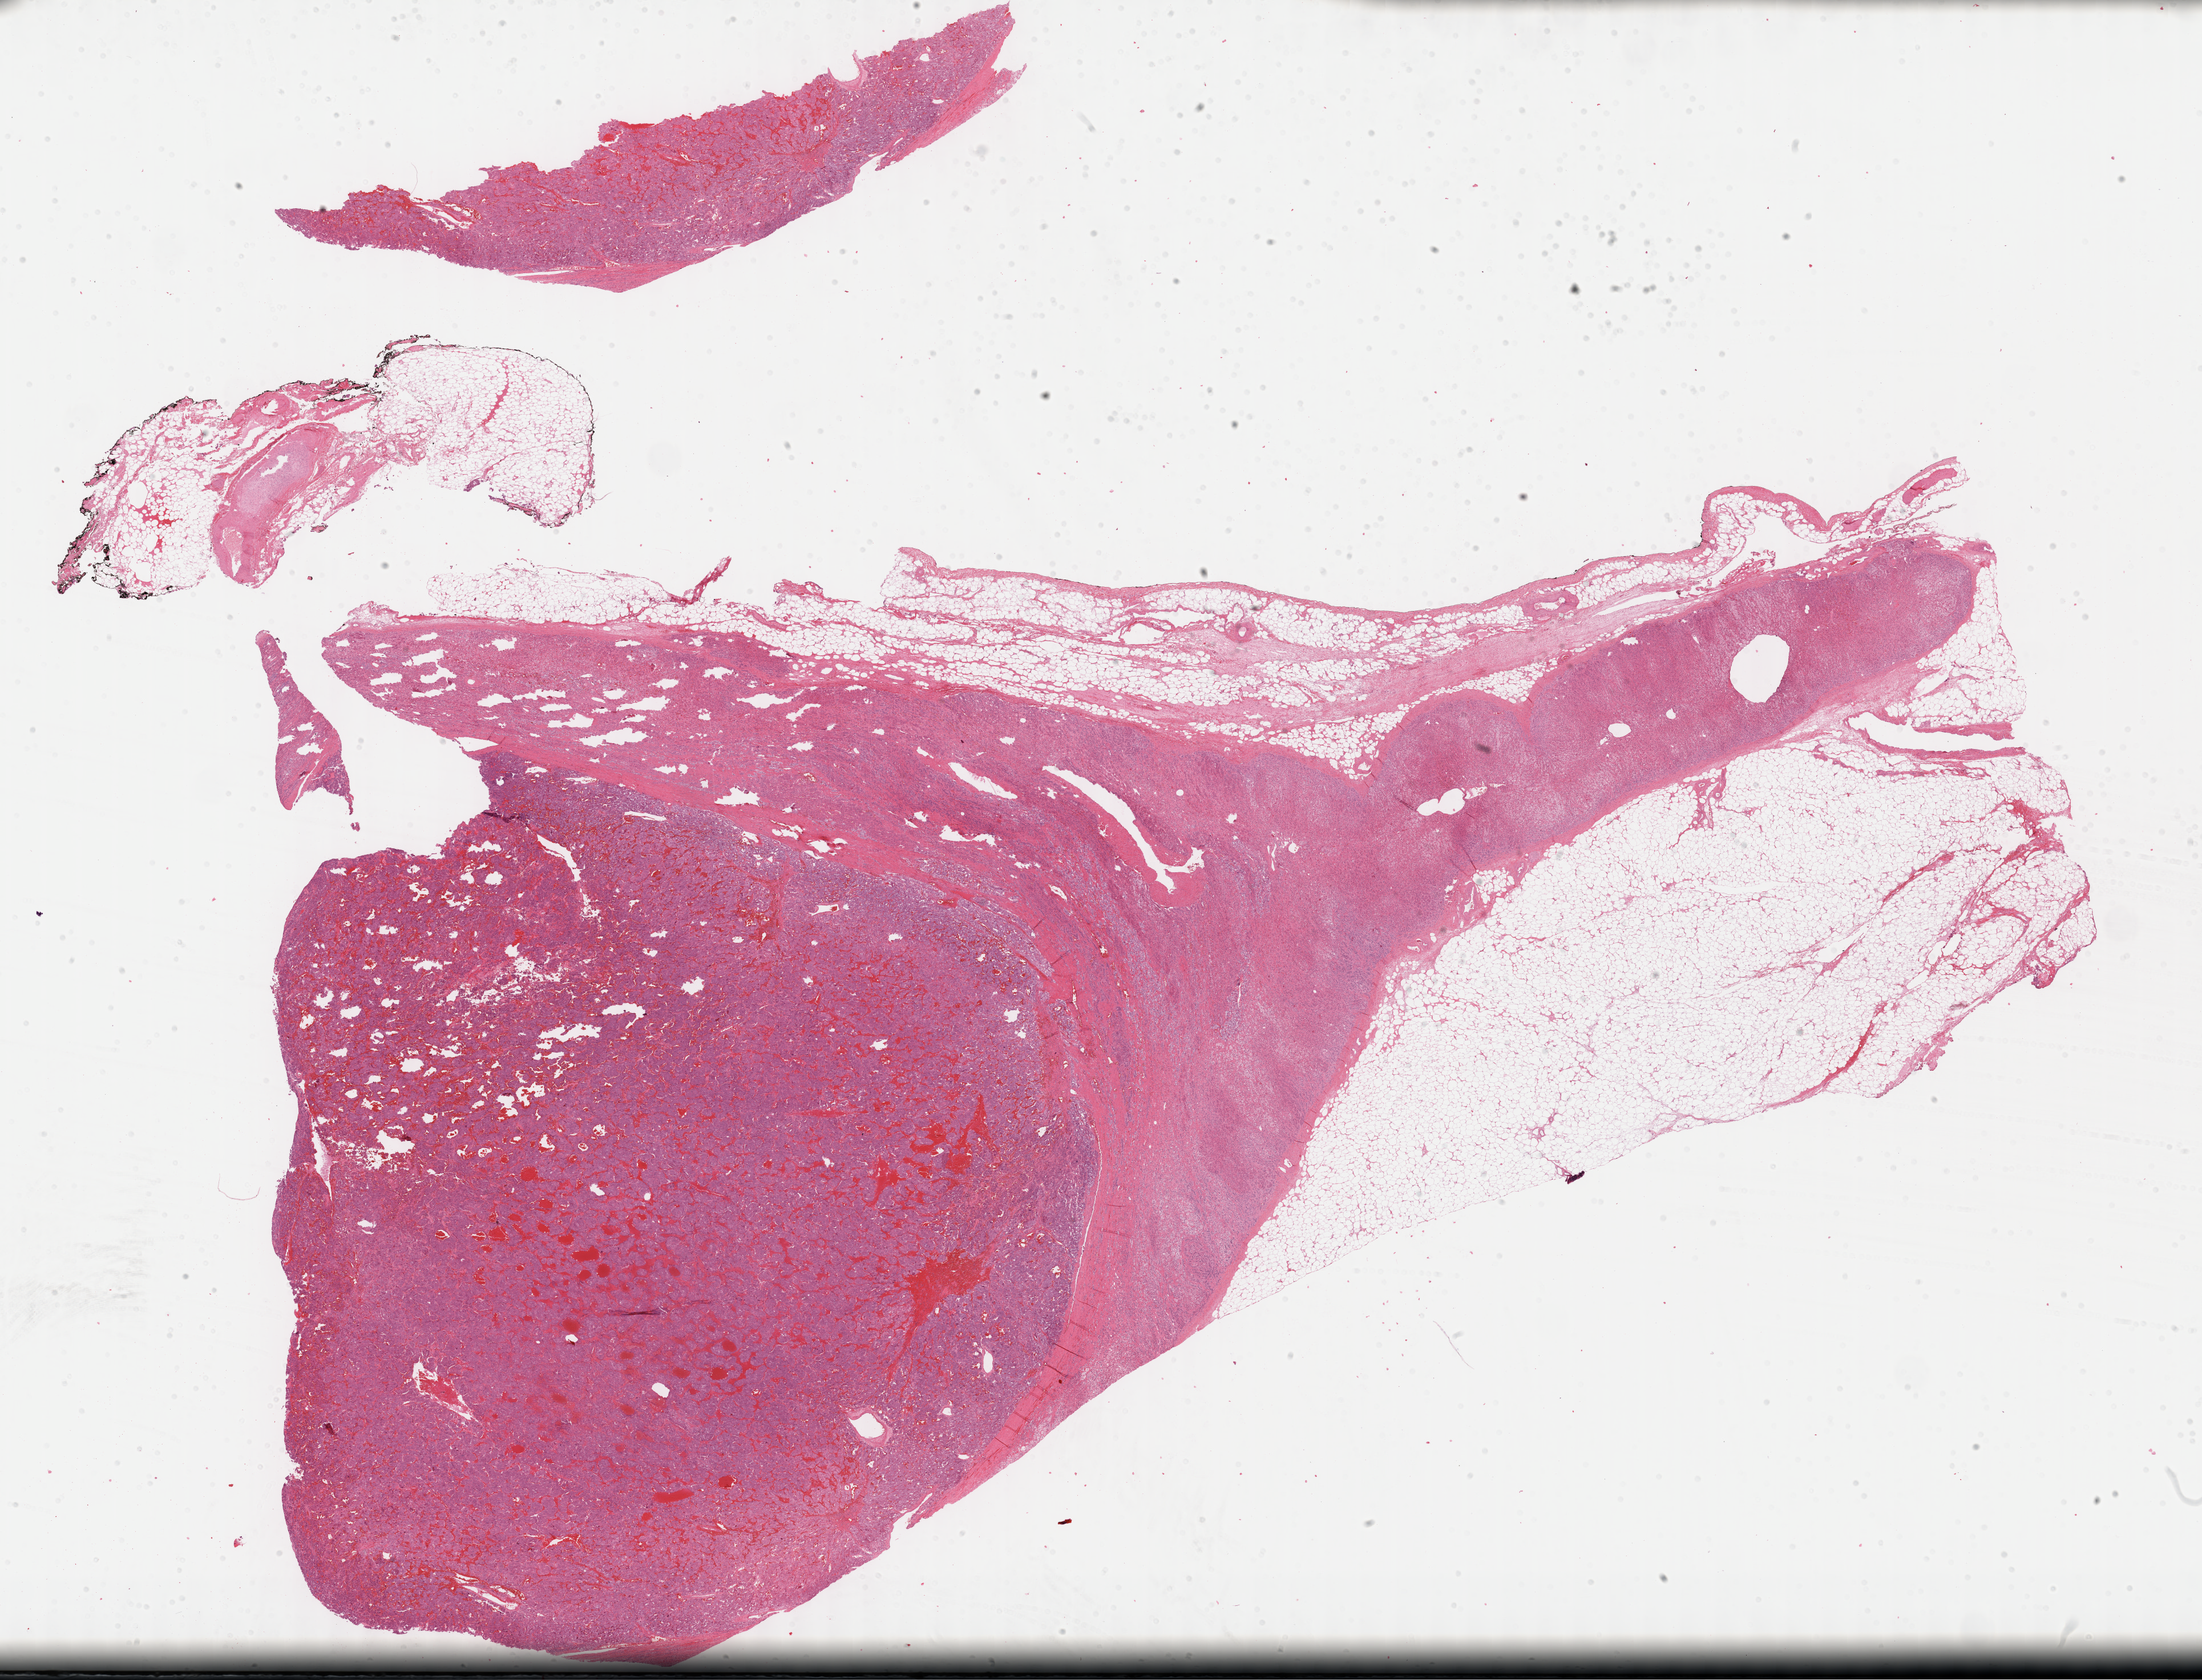
H&E whole-slide image — low-resolution overview of the scanned area, about 31.2 x 23.8 mm; formalin-fixed paraffin-embedded (FFPE) diagnostic section; sample: primary tumour, adrenal gland. Male patient; age at initial diagnosis 67 years.
* diagnosis: Pheochromocytoma, NOS